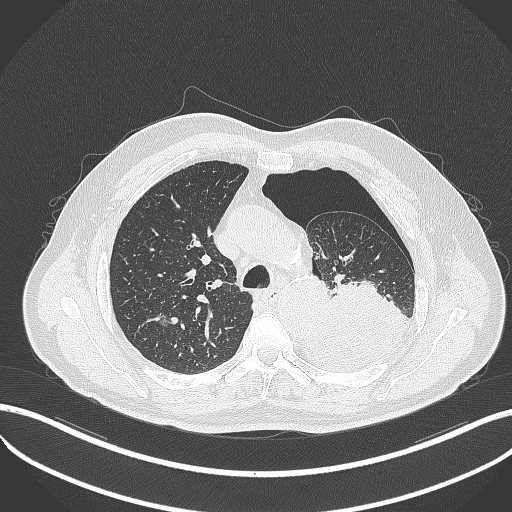
Chest CT, one axial slice; slice 366 of 464 in the series (ordered by position); reconstruction kernel B70f; lung window (W 1500 / L -600 HU); 512 × 512 image matrix. Patient: male, 76 years. Case-level facts recorded for this patient, not image findings: clinical TNM (as recorded): T3 N0 M1b.
Annotated regions visible in this slice (bounding box drawn by a radiologist):
- lung tumour (recorded histology: adenocarcinoma): bounding box (x1, y1, x2, y2) in pixels: (297, 282, 411, 371)